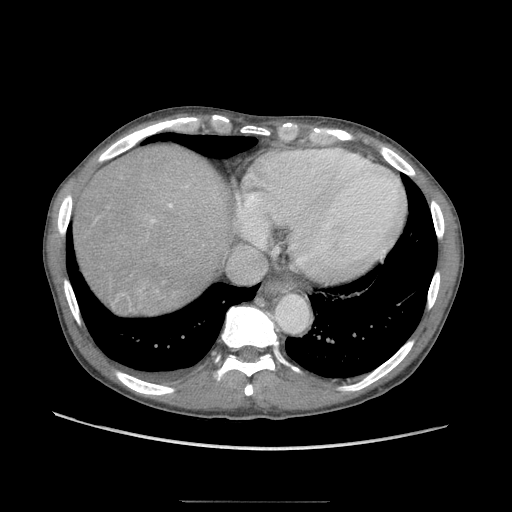
Contrast-enhanced abdominal CT (liver protocol), one axial slice; slice 88 of 103 in the series (ordered by position); reconstruction kernel STANDARD; 120 kVp; soft-tissue window (W 400 / L 40 HU); 2.5 mm slice thickness; 512 × 512 image matrix, field of view 380 × 380 mm. Case-level facts recorded for this patient, not image findings: diagnosis: hepatocellular carcinoma (patient treated with transarterial chemoembolisation; whether this scan precedes or follows treatment is not stated here); TNM stage (as recorded): Stage-IIIA; Child-Pugh class: A; tumour nodularity: multinodular; tumour size: 16 cm.
Annotated regions visible in this slice (semi-automatically segmented with operator editing):
- abdominal aorta: bounding box <276,295,308,331> (left, top, right, bottom; pixels)
- liver parenchyma outside the tumour (the mass and vessels are separate outlines, so this box may not span the whole liver): <74,144,218,306>
- mass: <112,290,130,310>